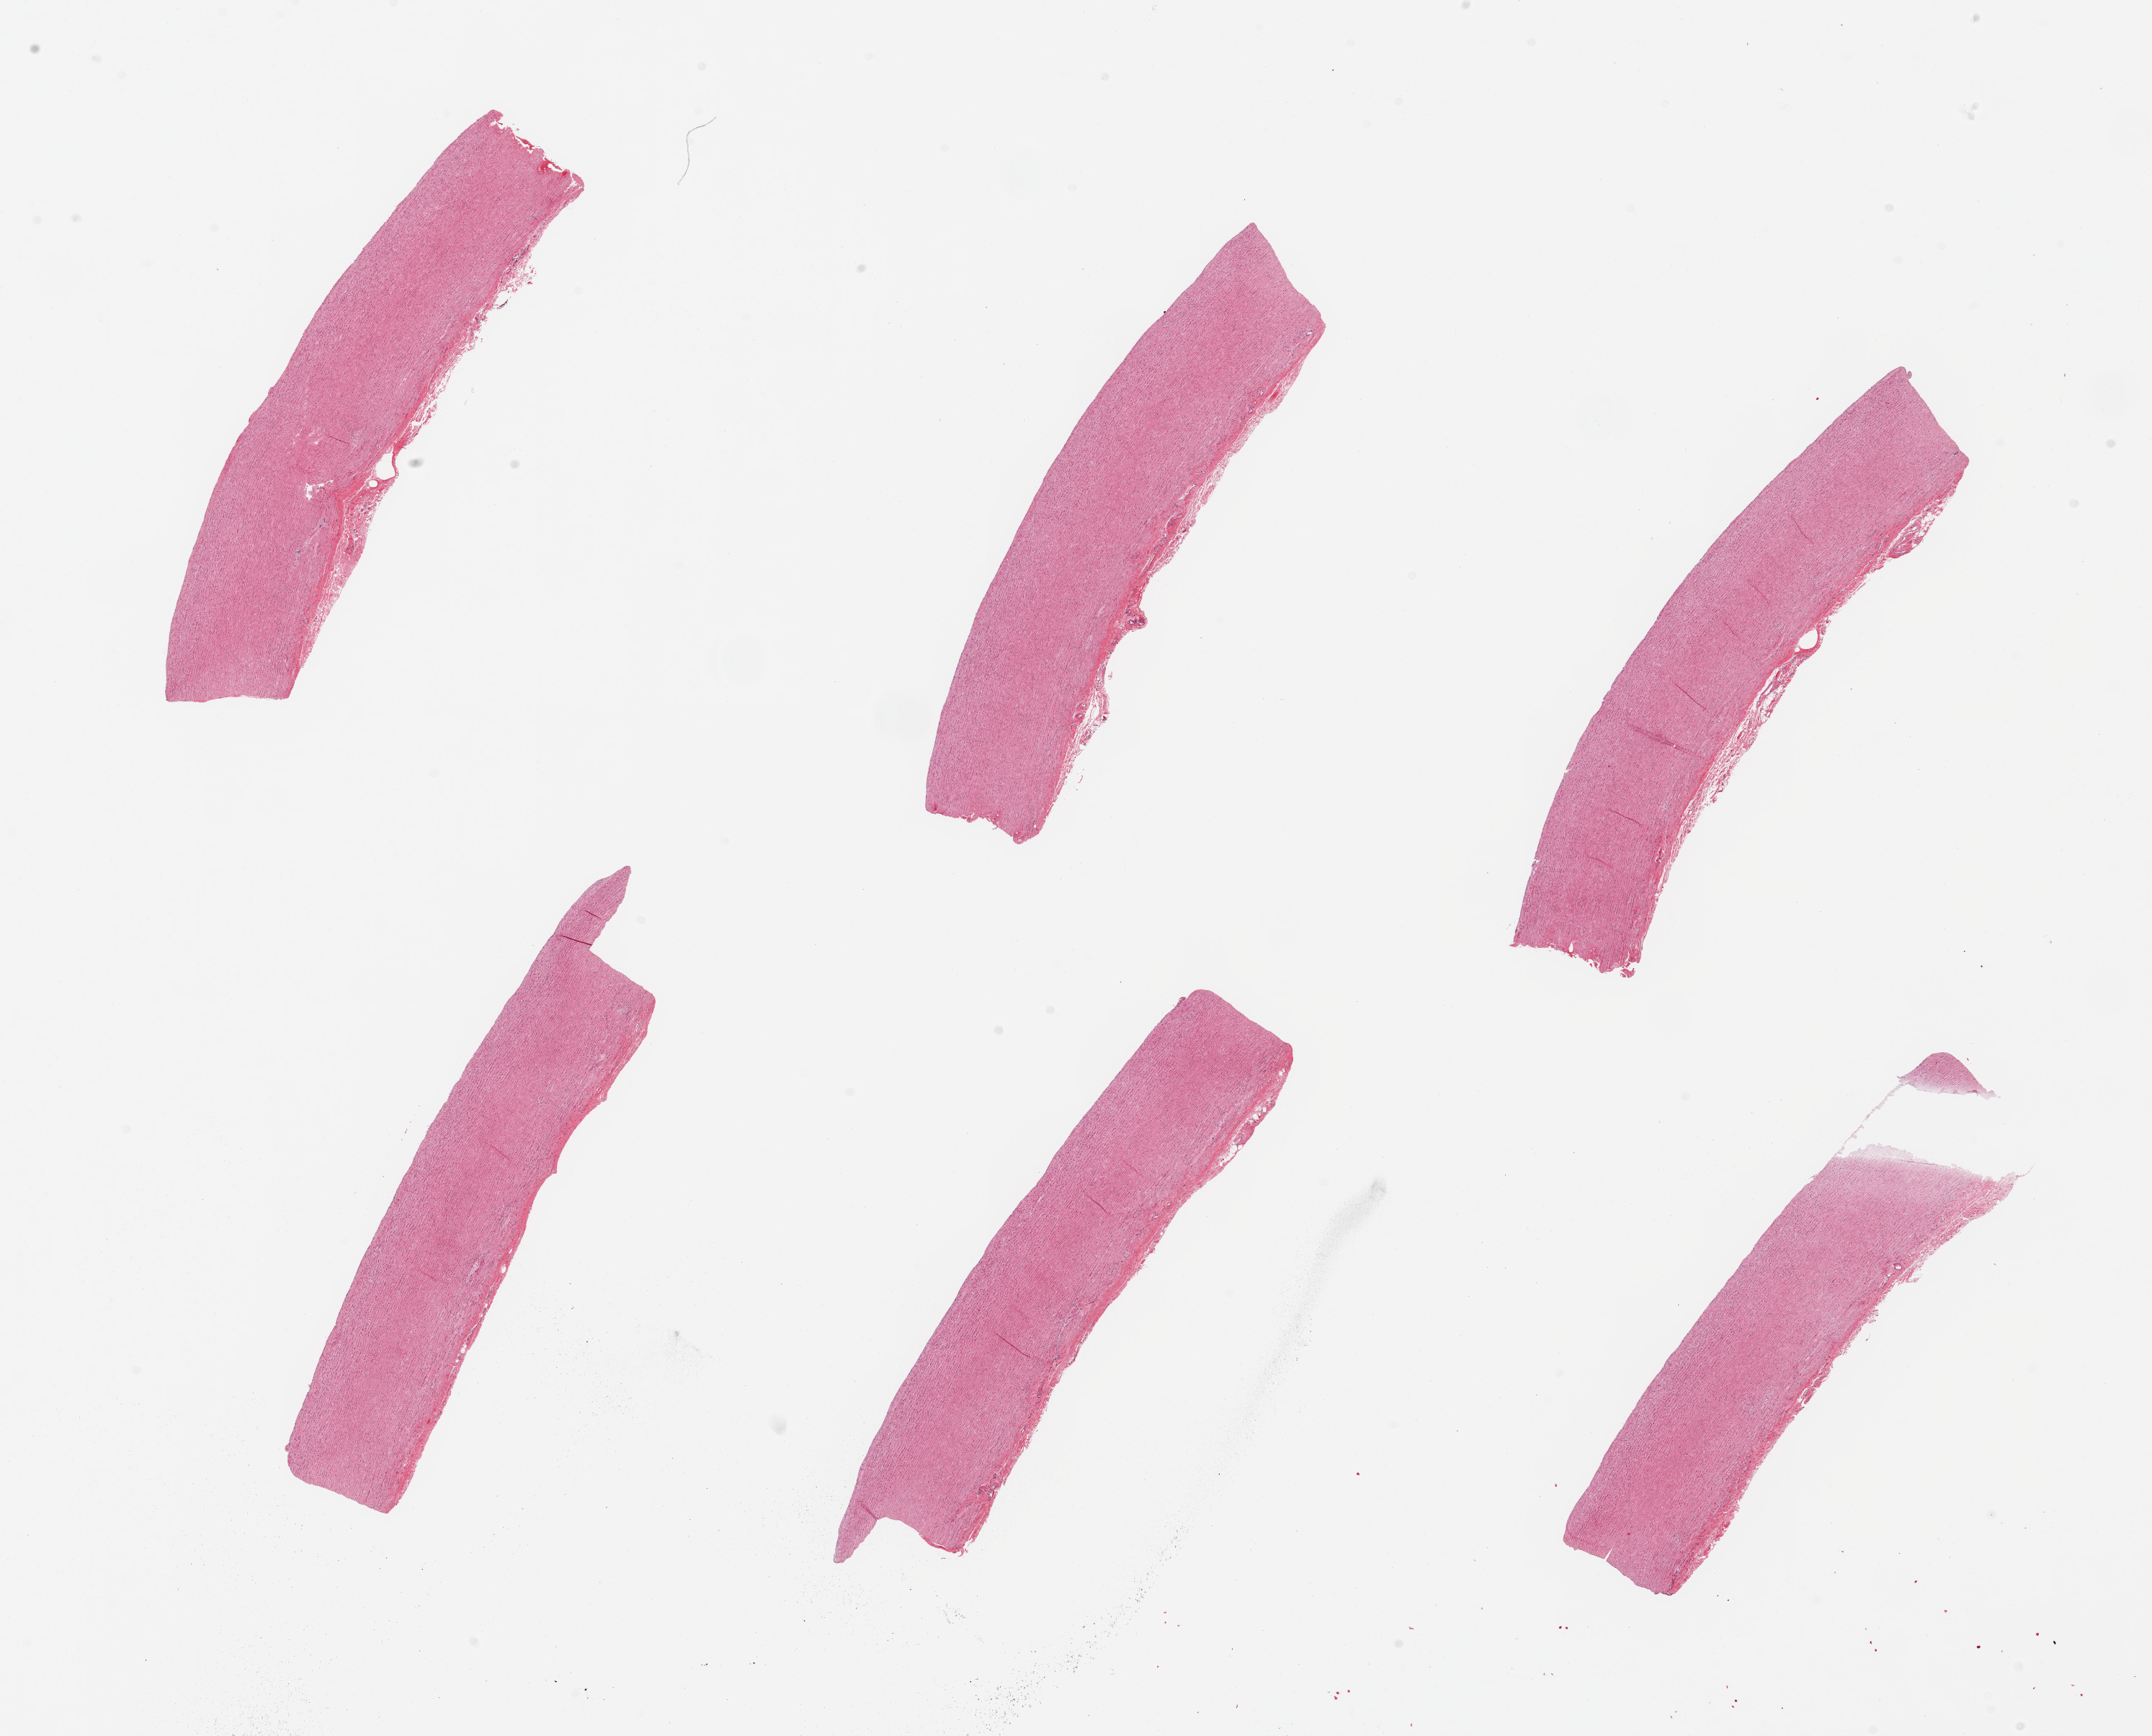
Hematoxylin and eosin (H&E) whole-slide image, brightfield — shown as a low-resolution overview of the whole scanned area (about 23.6 x 19.1 mm, slide scanned at 20x). PAXgene-fixed paraffin-embedded (PFPE) section. Section of aorta (target tissue). Donor tissue sample. Male donor.
Review note (as recorded): 6 pieces, minimal atherosis.